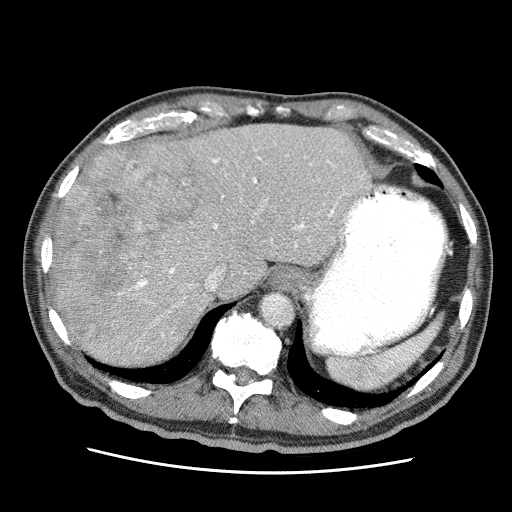
Contrast-enhanced abdominal CT (liver protocol), one axial slice. Position 48 of 75 along the scan axis. Reconstruction kernel STANDARD. Soft-tissue window (W 400 / L 40 HU). 2.5 mm slice thickness. 512 × 512 image matrix, field of view 360 × 360 mm. From the clinical record (not read from this slice): diagnosis: hepatocellular carcinoma (patient treated with transarterial chemoembolisation; whether this scan precedes or follows treatment is not stated here); TNM stage (as recorded): Stage-IIIA; Child-Pugh class: A; tumour differentiation: well differentiated.
Outlined on this slice (semi-automatic segmentation, software-assisted and operator-edited):
- abdominal aorta: bounding box <261,293,294,327> (left, top, right, bottom; pixels)
- liver parenchyma outside the tumour (the mass and vessels are separate outlines, so this box may not span the whole liver): <52,124,372,364>
- mass: <56,148,214,343>
- liver vessels: <118,143,365,350>